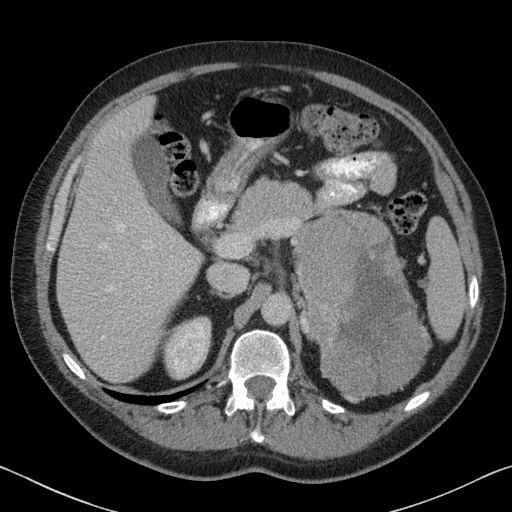
Contrast-enhanced abdominal CT, one axial slice. Slice 50 of 88 in the series (ordered by position). Reconstruction kernel B31f. 120 kVp. Intravenous contrast given. Soft-tissue window (W 400 / L 40 HU). 3 mm slice thickness. 512 × 512 image matrix, field of view 366 × 366 mm. Male patient, age 51 years. From the clinical record (not read from this slice): diagnosis: adrenocortical carcinoma; tumour side: left adrenal; tumour size at pathology: 16.5 cm; Ki-67 index: 30 %; stage (as recorded): 2.
Structures marked on this image (semi-automatic segmentation, software-assisted and operator-edited):
- mass: bounding box <294,213,429,400> (left, top, right, bottom; pixels)